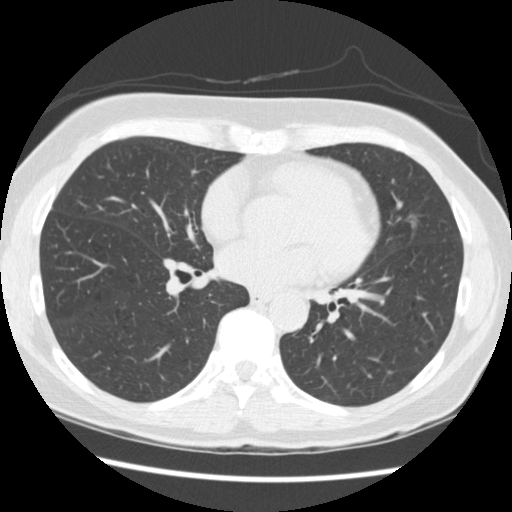
Chest CT (low-dose screening protocol), one axial image; third screening round (two years after baseline); lung window (W 1500 / L -600 HU); standard (soft-tissue) reconstruction kernel (STANDARD); 120 kVp; slice 138 of 262 in the series. Female participant, aged 60 years at enrolment.
- Lesion marked by an expert reader, bounding box <391,206,433,251> (left, top, right, bottom; pixels).
- Reader record for this screening exam (exam-level; its link to the box is not recorded): non-calcified nodule or mass ≥4 mm, lingula, 6 × 5 mm, smooth margins, soft tissue attenuation, pre-existing on the prior screen: yes; interval growth: yes.
- Later outcome: lung cancer diagnosed 209 days after this screen — adenocarcinoma, NOS, lingula, poorly differentiated (G3), stage IA (AJCC 6th edition), 6 mm at pathology.